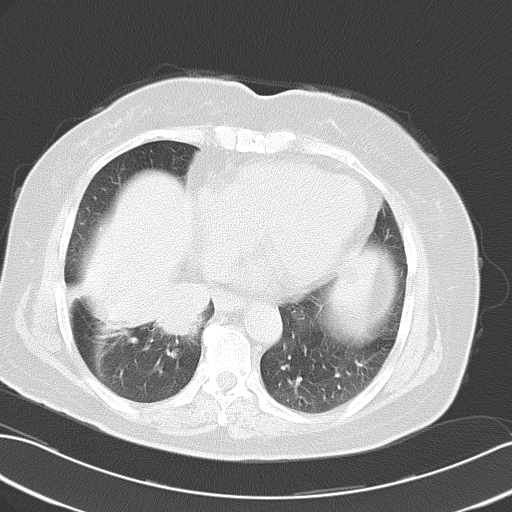
Chest CT, one axial slice. Position 18 of 50 along the scan axis. Reconstruction kernel B70f. 120 kVp. Lung window (W 1500 / L -600 HU). 512 × 512 image matrix, field of view 353 × 353 mm. Female patient, age 63 years. Case-level facts recorded for this patient, not image findings: clinical TNM (as recorded): T3 N0 M0.
Structures marked on this image (bounding box drawn by a radiologist):
- lung tumour (recorded histology: adenocarcinoma): bounding box [x1, y1, x2, y2] px = [160, 281, 213, 336]